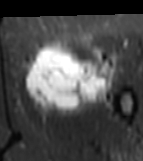
MRI of an extremity soft-tissue mass, one axial slice; slice 28 of 81 in the series (ordered by position); STIR; MR volume resampled by the dataset authors to the PET/CT grid (not the native acquisition matrix); 143 × 161 image matrix. Female patient. Case-level facts recorded for this patient, not image findings: histological type: myxofibrosarcoma; grade: intermediate; site of the primary tumour: left thigh.
Structures marked on this image (expert contour drawn on MRI and transferred to this co-registered scan by the dataset authors):
- gross tumour volume including surrounding oedema: bounding box [x1, y1, x2, y2] px = [24, 44, 116, 116]
- gross tumour volume (mass): [26, 44, 114, 109]